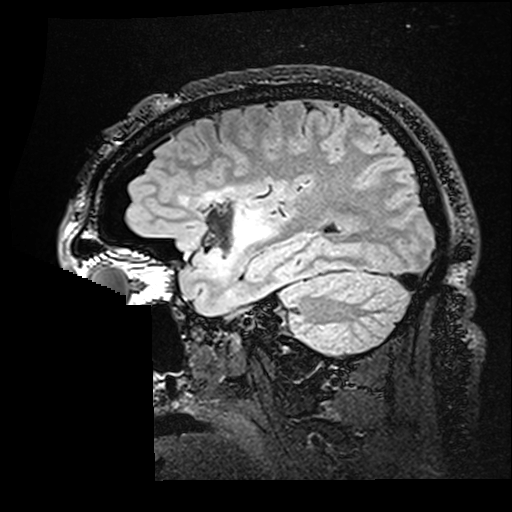
Brain MRI from a brain-tumour surgery series, one sagittal slice; position 122 of 176 along the scan axis; T2 FLAIR; 1 mm slice thickness; 512 × 512 image matrix, field of view 250 × 250 mm. Case-level facts recorded for this patient, not image findings: histopathology: Astrocytoma; WHO grade: 2; IDH mutation: yes; tumour location: Right Insular.
Annotated regions visible in this slice (manually delineated by an expert):
- residual tumour: bounding box (x1, y1, x2, y2) in pixels: (182, 190, 268, 247)